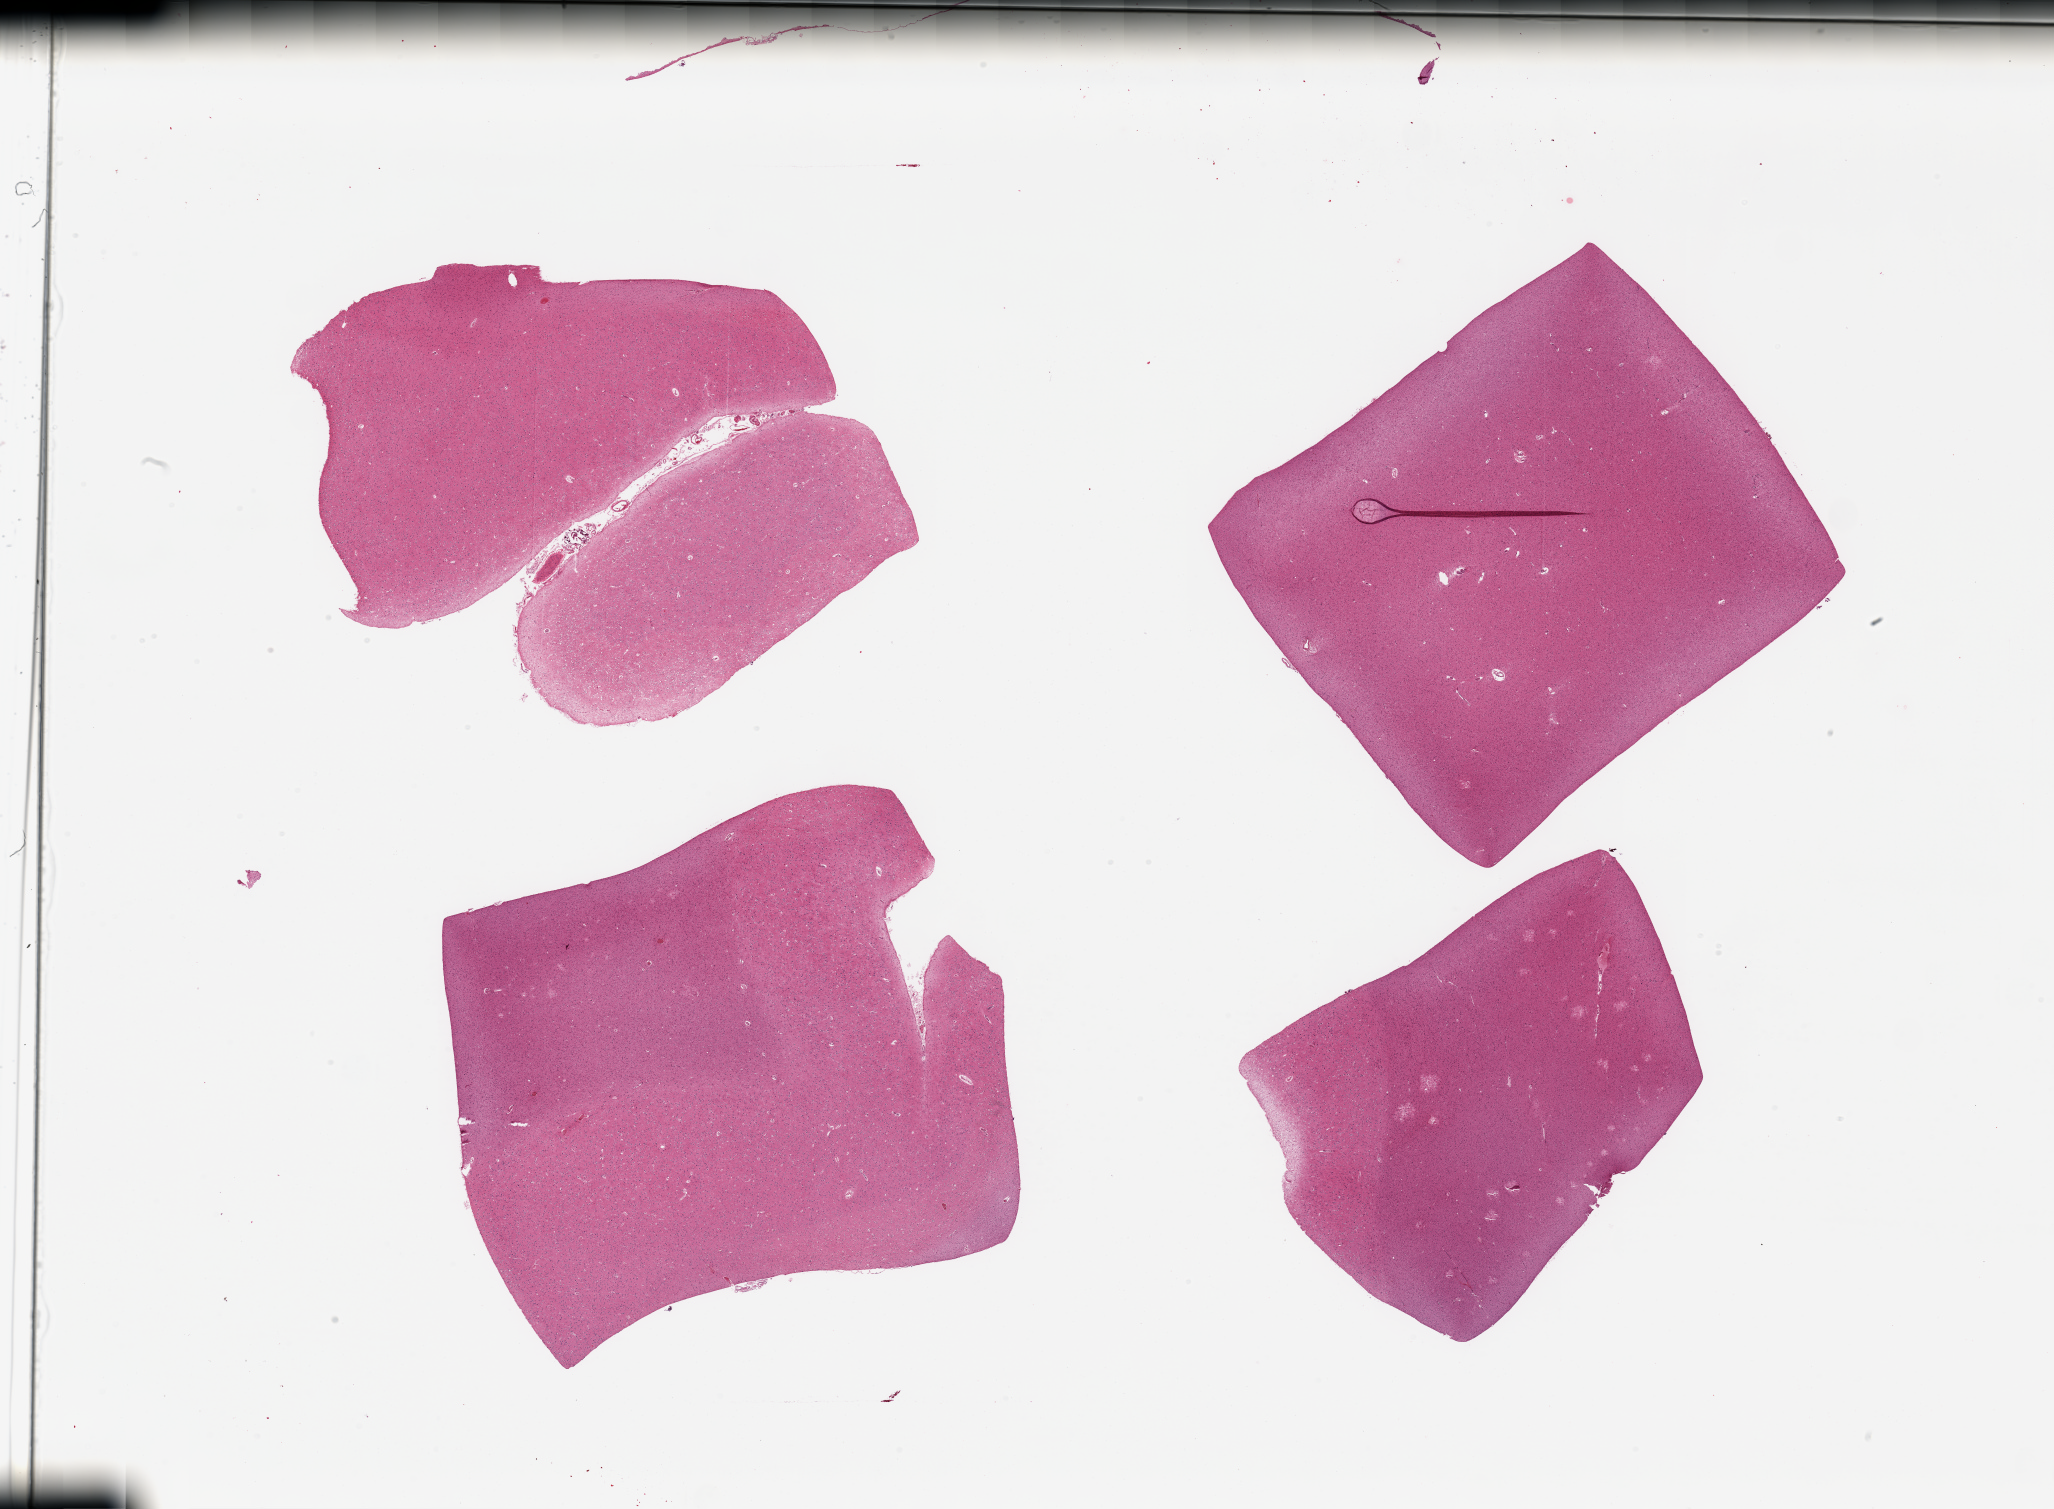
Haematoxylin and eosin whole-slide image — a low-resolution overview of the entire scanned area, about 32.5 x 23.9 mm (from a 20x scan). PAXgene-fixed, paraffin-embedded tissue. Target tissue: cerebral cortex. Donor tissue sample.
• review note (as recorded): 4 pieces; more white matter than usual